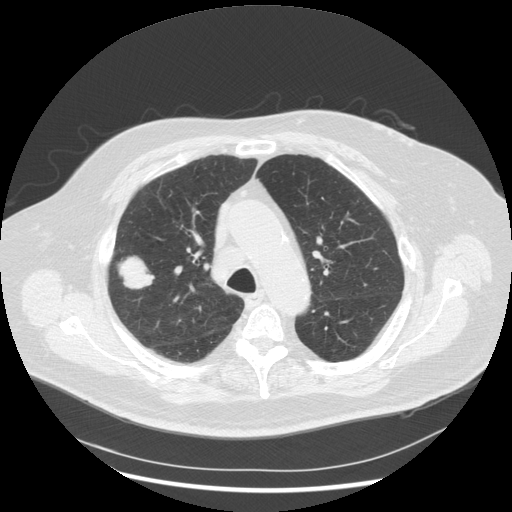
Low-dose screening chest CT, one axial slice; slice 198 of 263 in the series (ordered by position); 120 kVp; lung window (W 1500 / L -600 HU); 2.5 mm slice thickness; 512 × 512 image matrix.
Outlined on this slice (manually delineated by an expert):
- lesion 1 (tumor, upper lobe of right lung): bounding box [x1, y1, x2, y2] px = [119, 257, 154, 289]